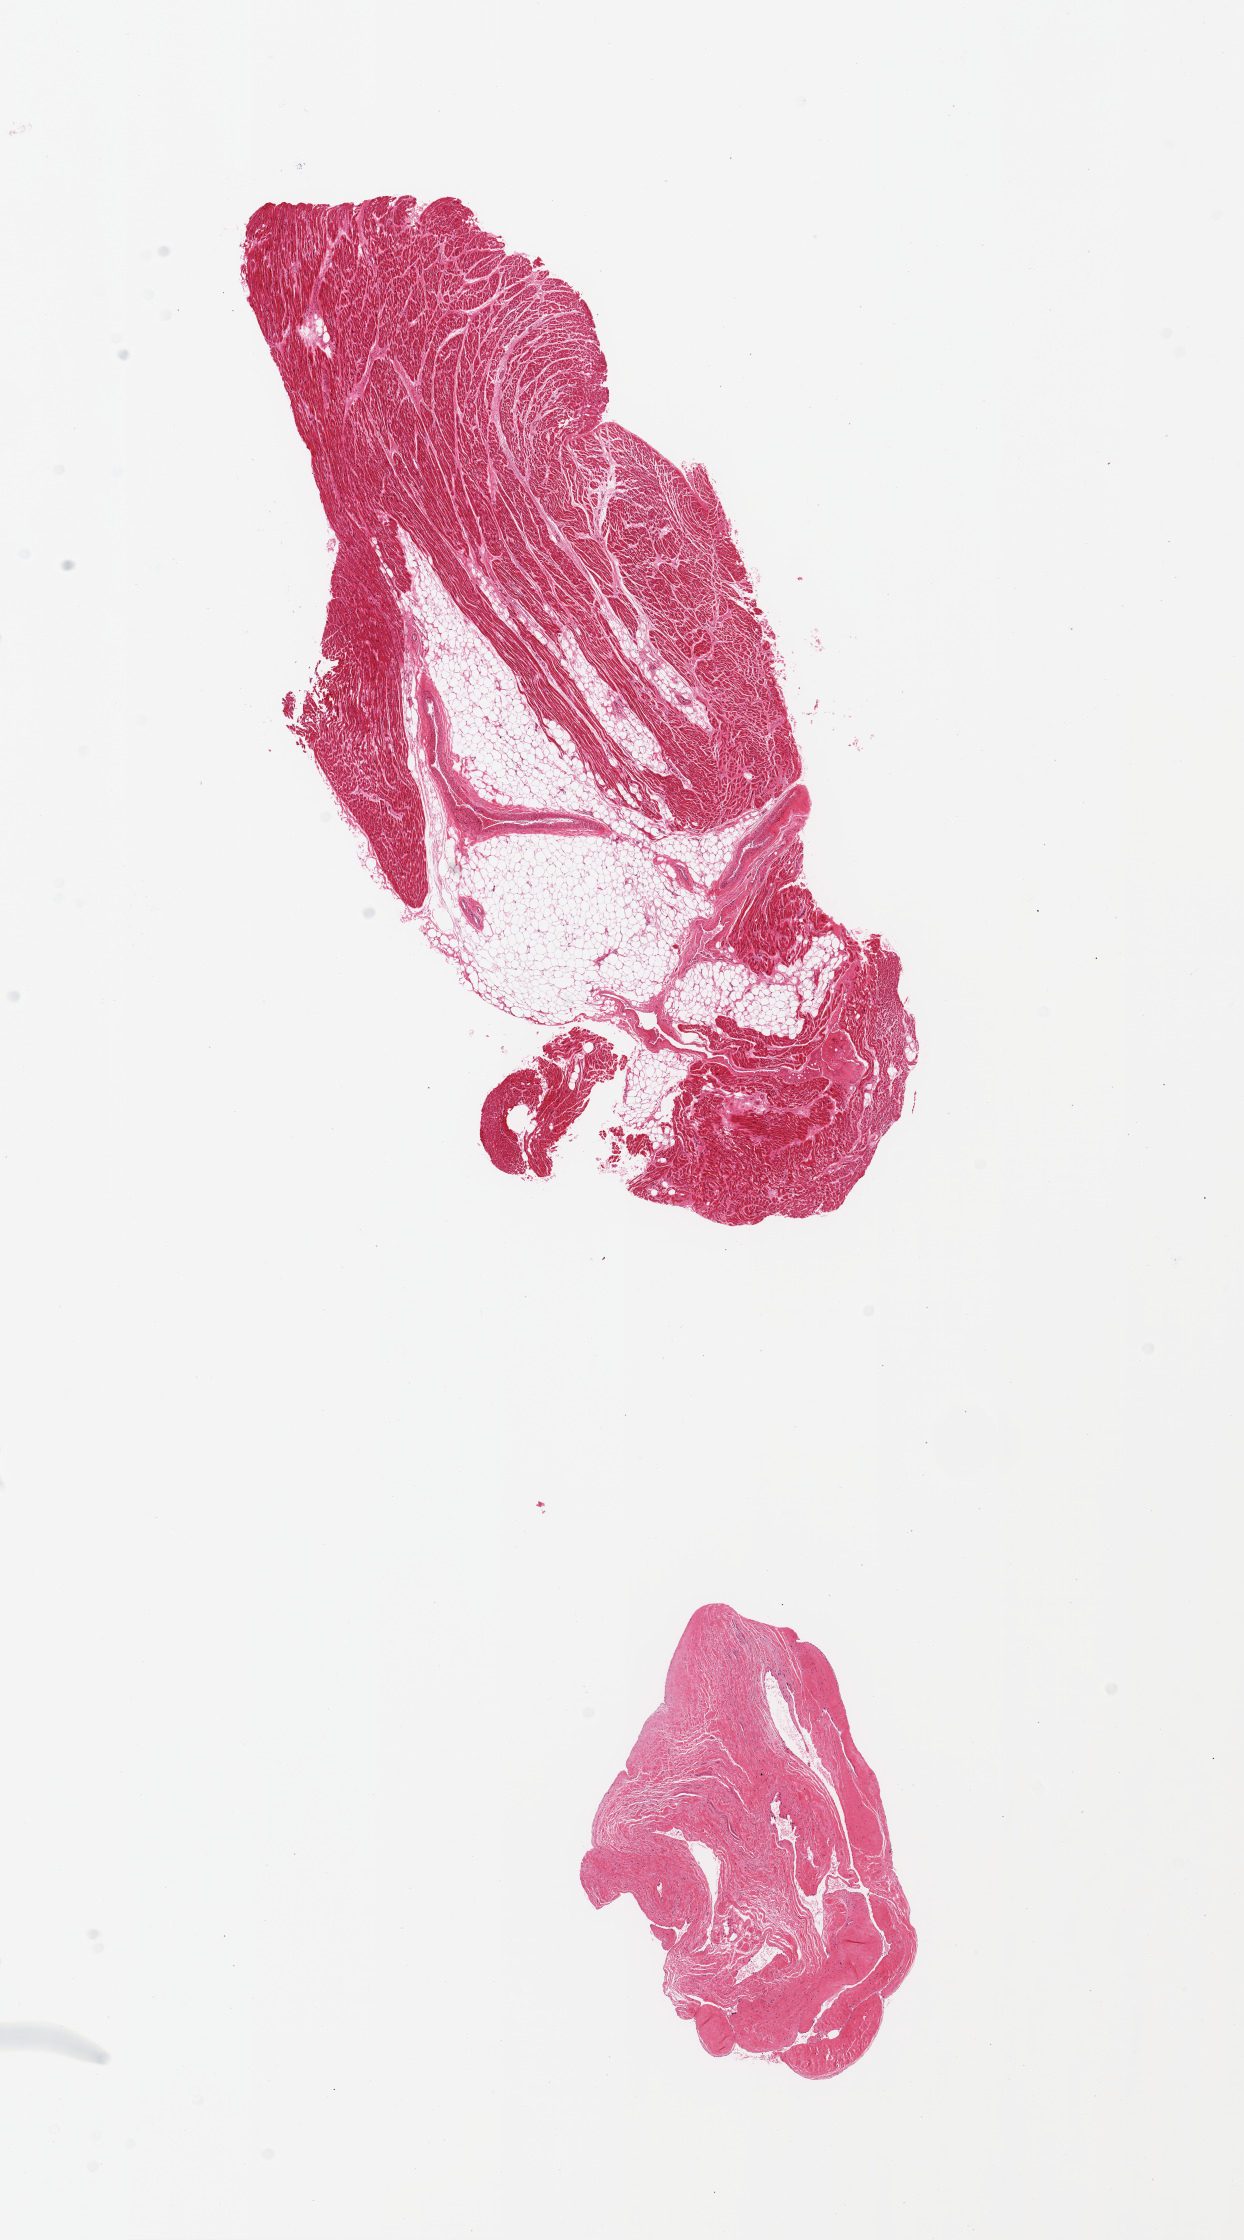
Haematoxylin and eosin whole-slide image, brightfield, whole scanned area (about 9.8 x 17.7 mm) shown as a low-resolution overview, PAXgene-fixed paraffin-embedded (PFPE) section, sampled site (target tissue): coronary artery, tissue donor sample. Donor: female.
Pathologist's review note for this sample: 2 pieces, no artery, fragments of mycocardium, pericardium, epicardial fat.